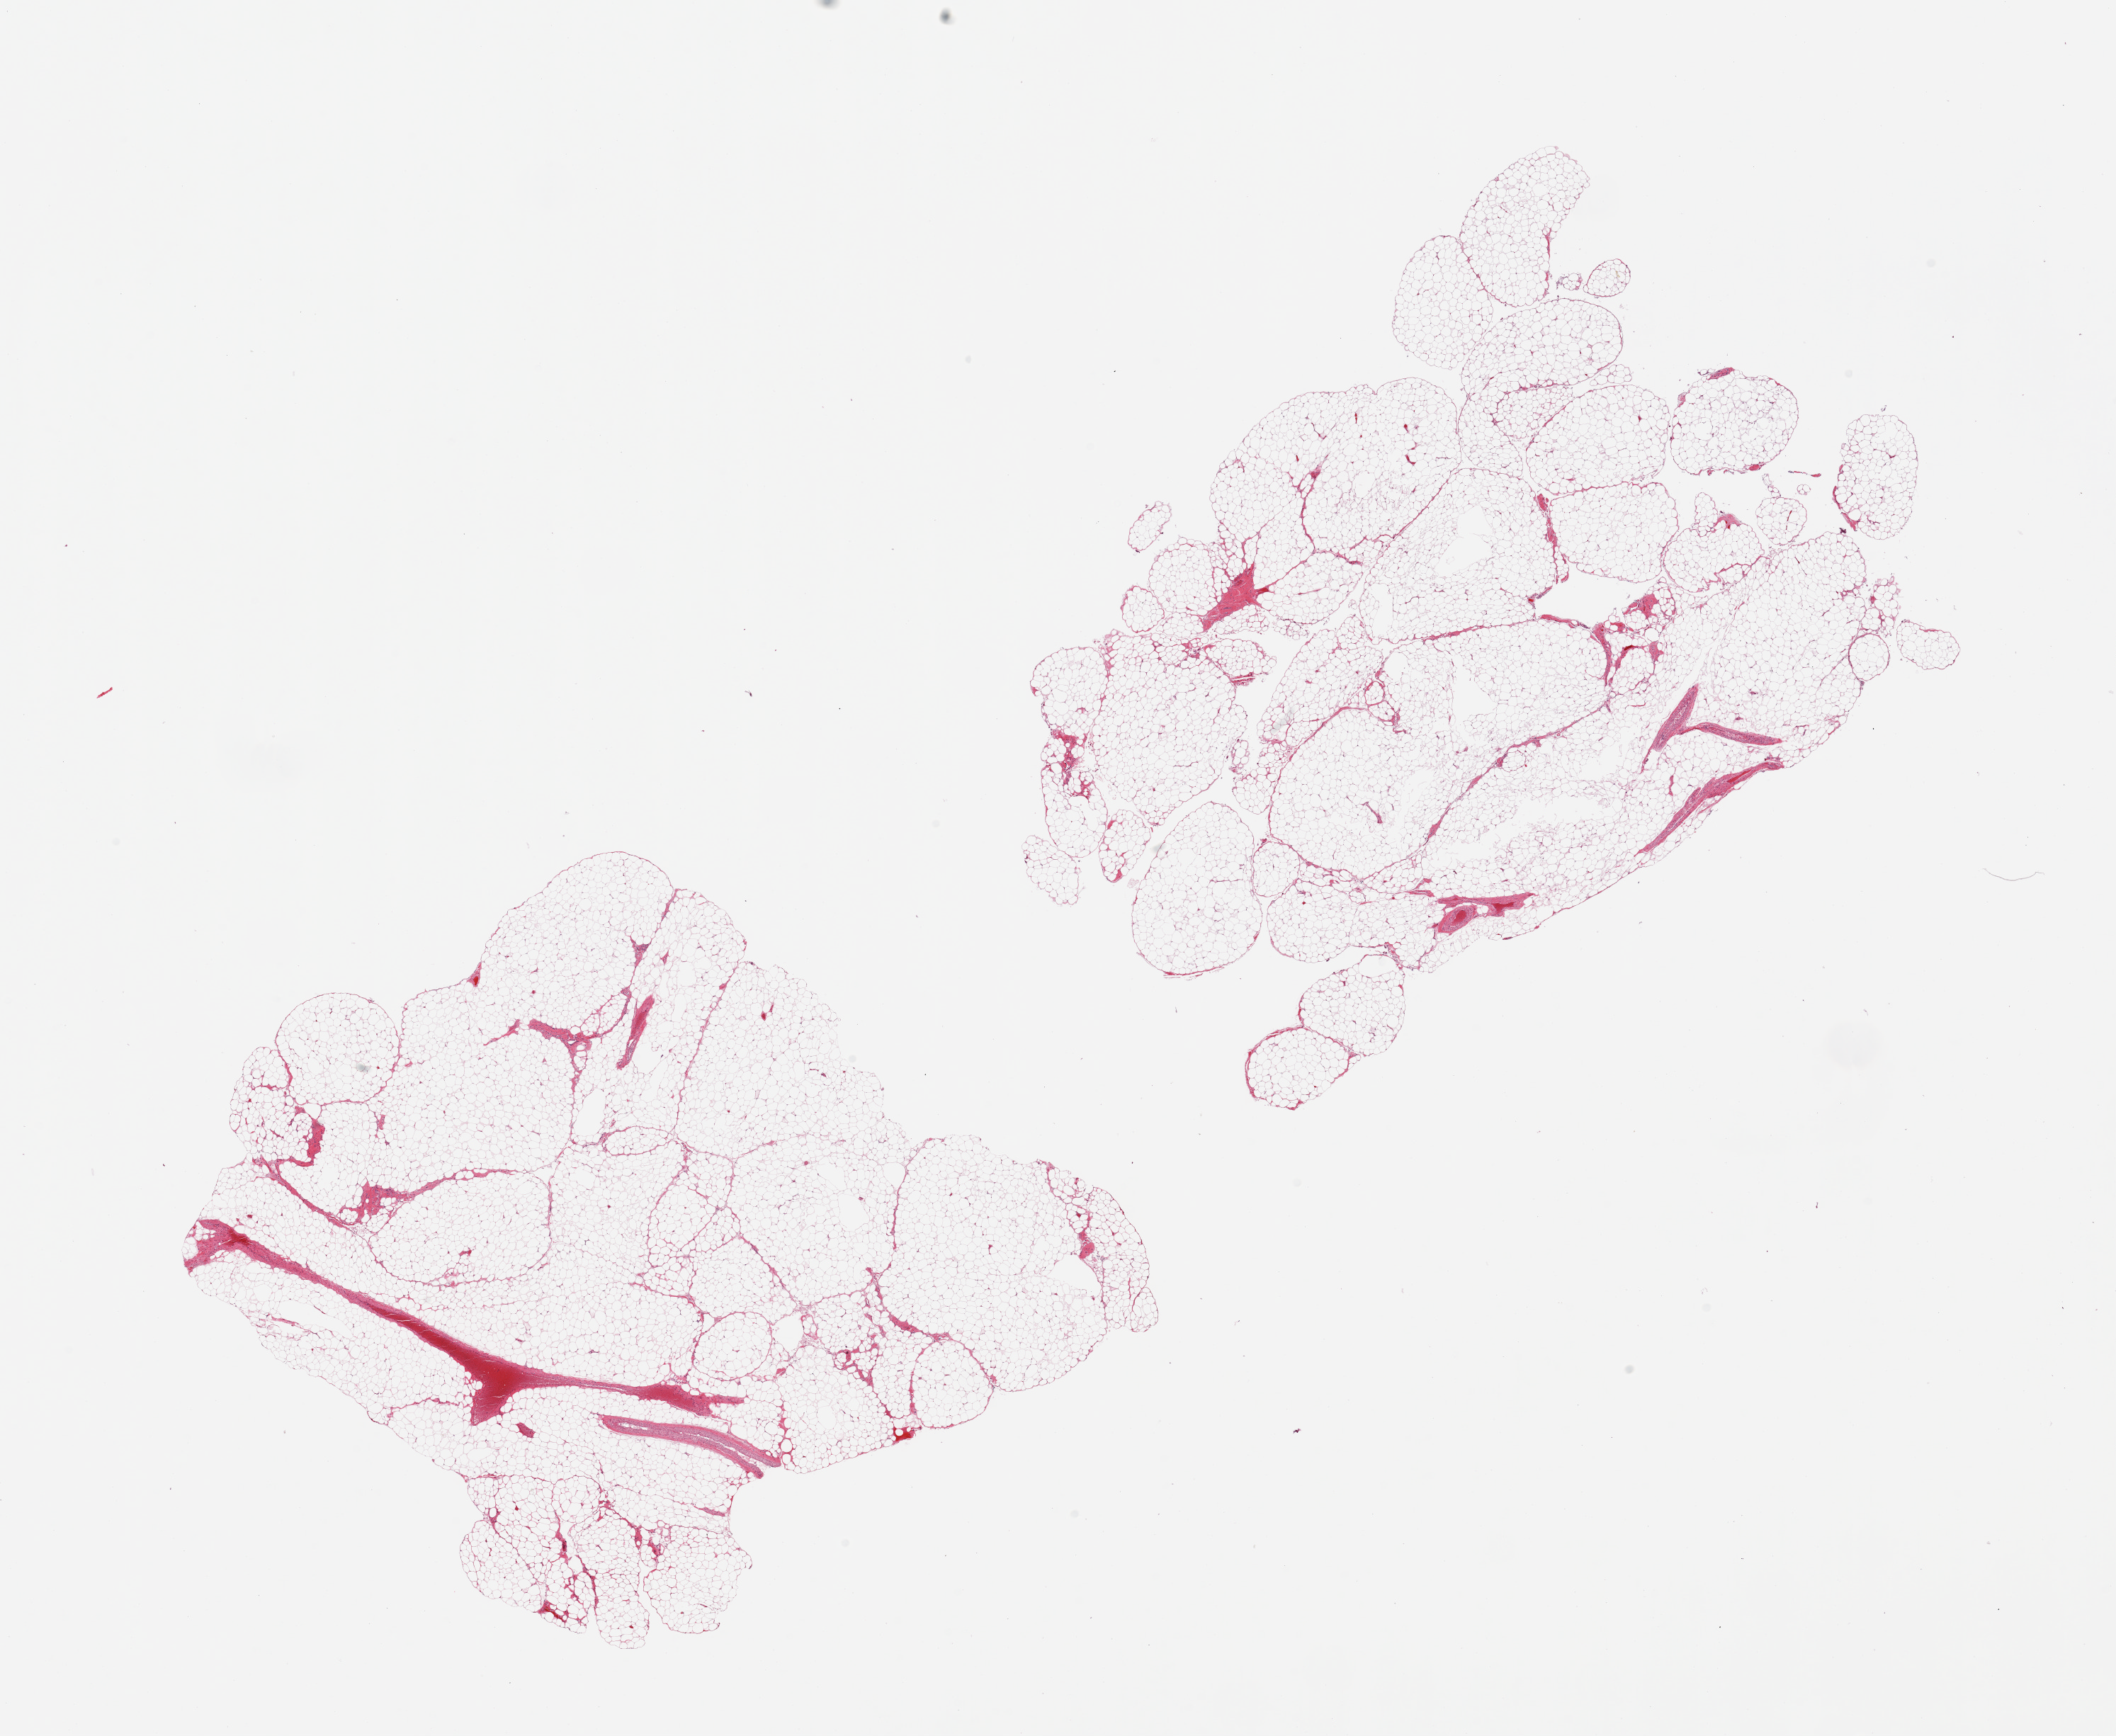
Whole-slide image, haematoxylin and eosin stain — low-resolution overview of the scanned area, about 23.6 x 19.4 mm; PAXgene-fixed paraffin-embedded (PFPE) section; section of omentum (target tissue); donor tissue sample. Donor: male.
- pathologist's review note for this sample: 2 pieces